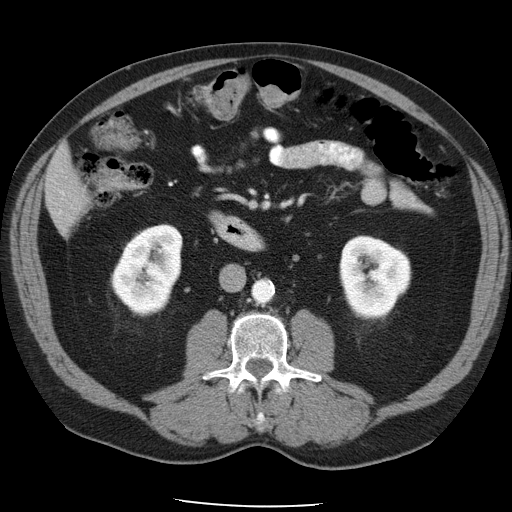
Contrast-enhanced abdominal CT, one axial slice. Position 15 of 49 along the scan axis. 120 kVp. Intravenous contrast given. Soft-tissue window (W 400 / L 40 HU). 5 mm slice thickness. 512 × 512 image matrix, field of view 395 × 395 mm. Male patient, age 68 years. Case-level facts recorded for this patient, not image findings: diagnosis: colorectal cancer liver metastases, imaged before liver resection.
Structures marked on this image (expert manual segmentation):
- liver: bounding box [x1, y1, x2, y2] px = [46, 149, 86, 229]
- portal vein (with intrahepatic branches): [60, 212, 62, 214]